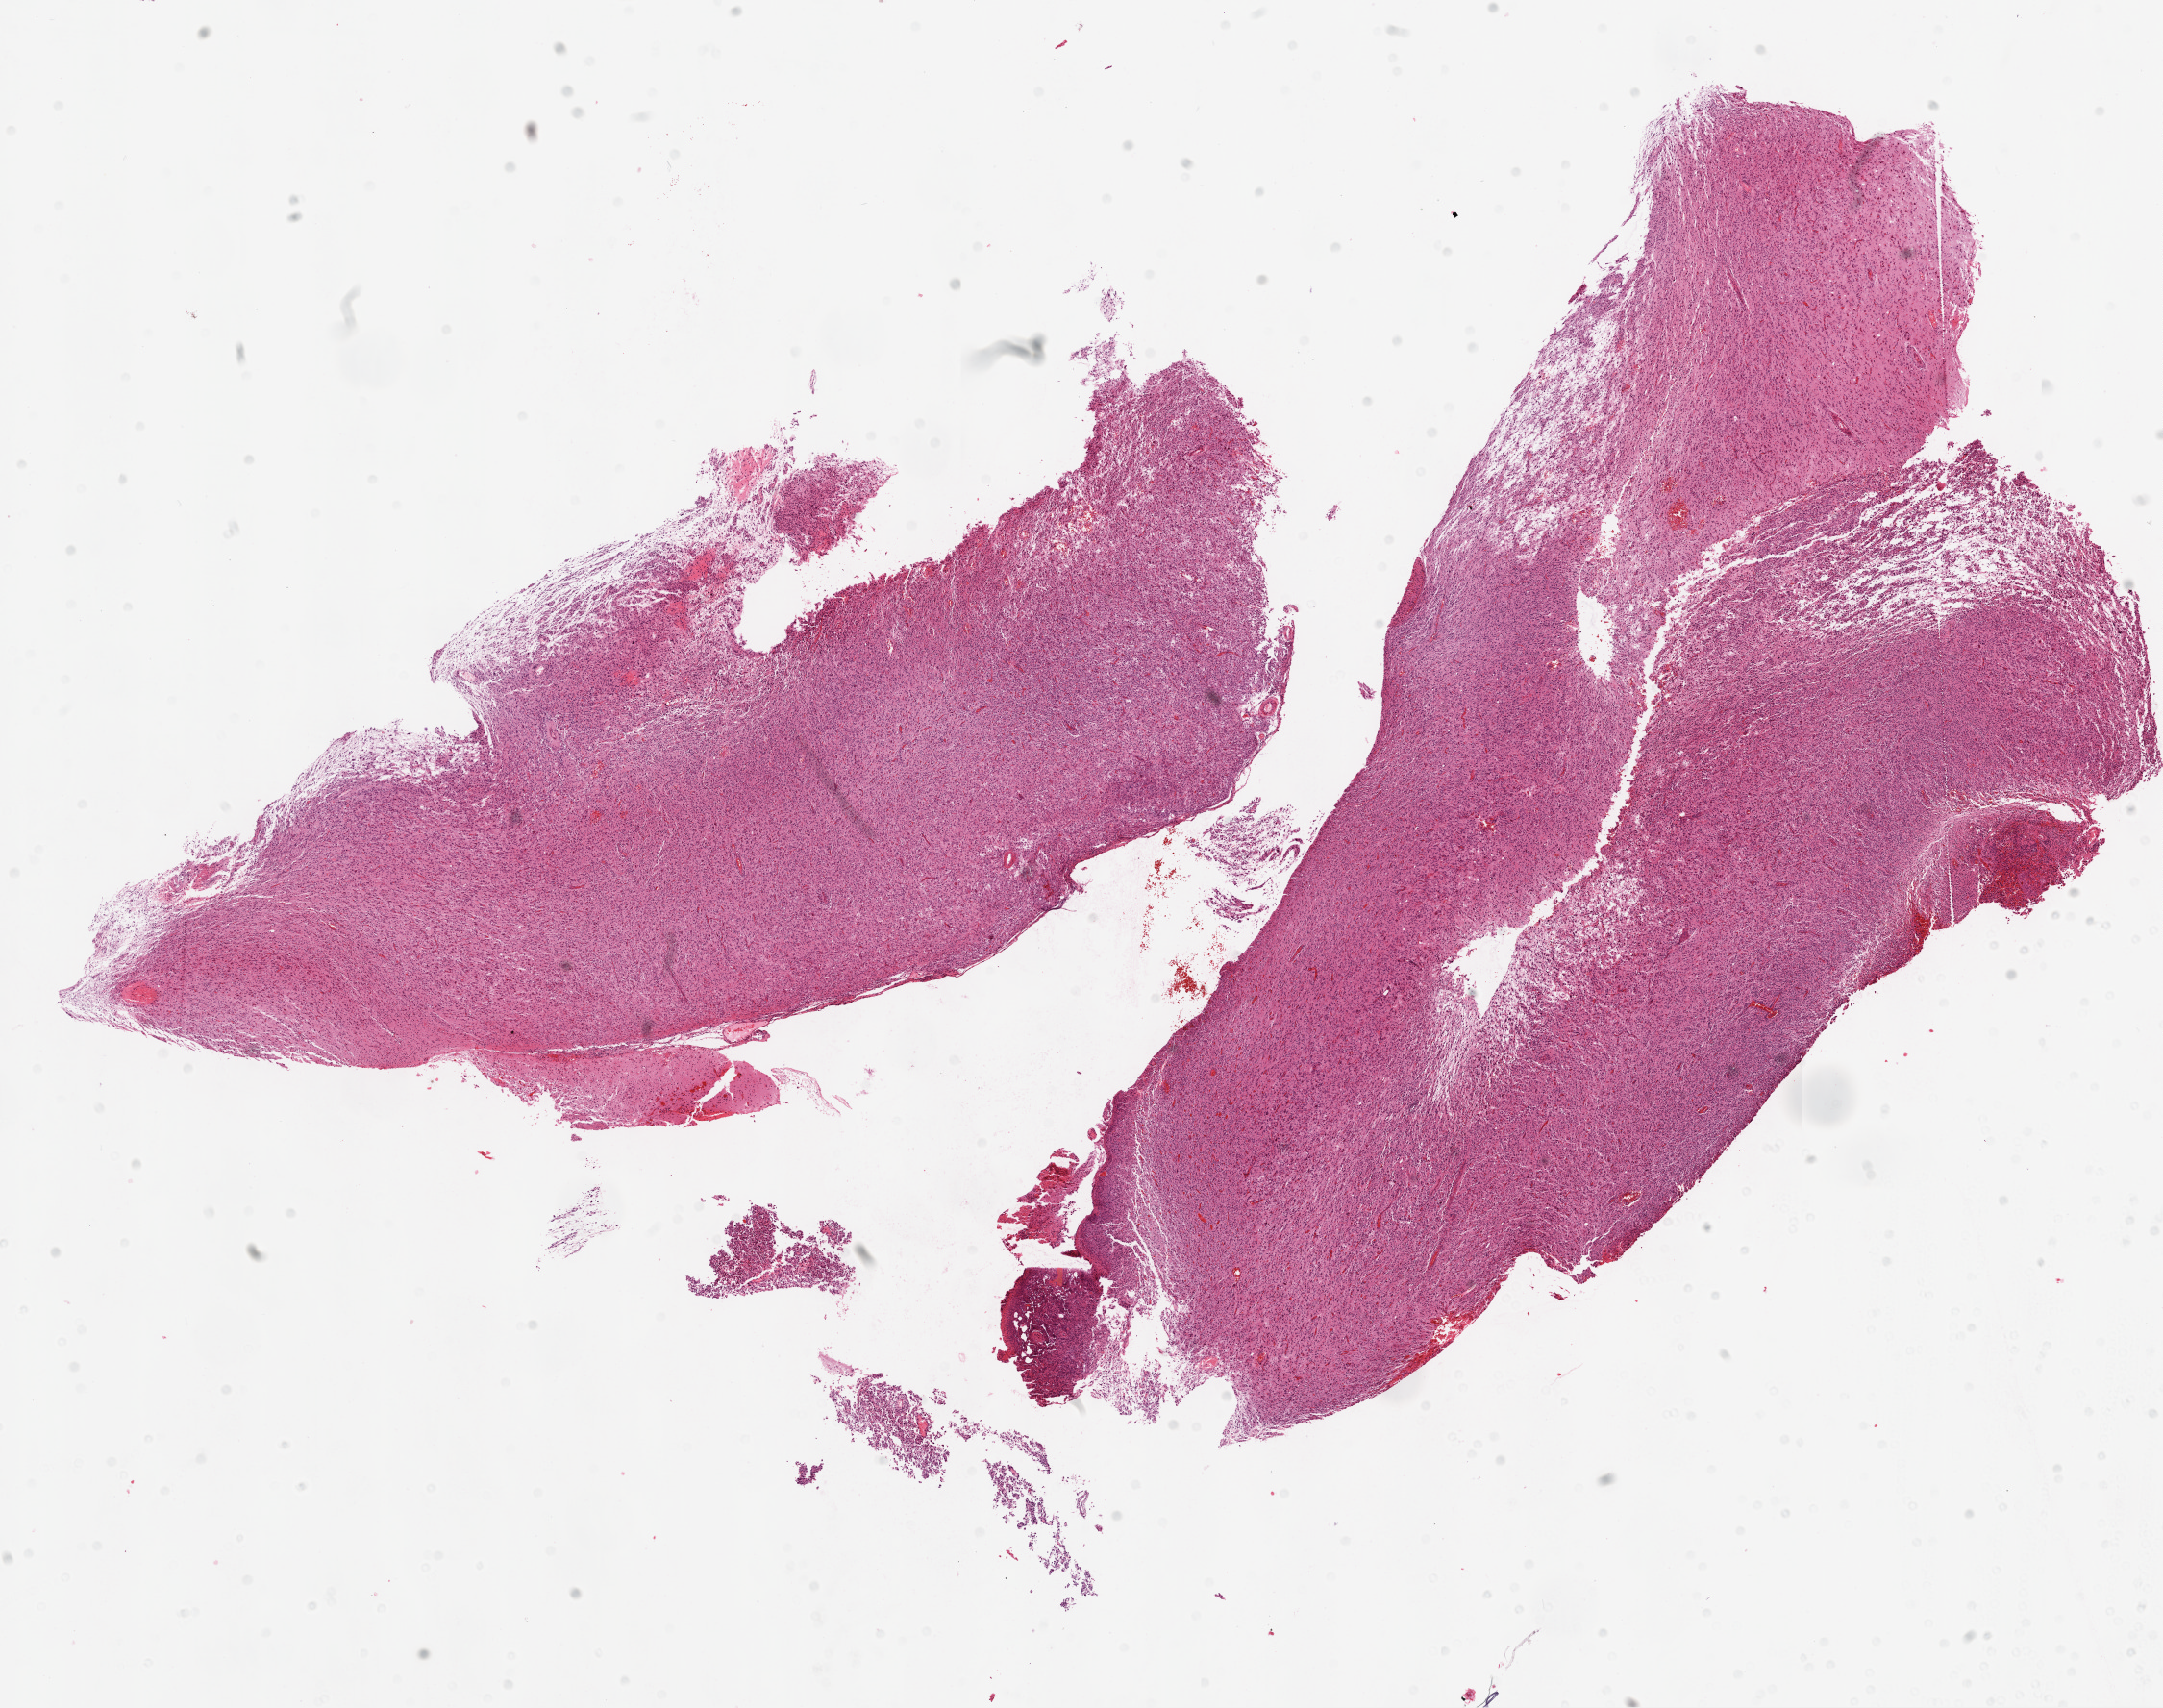
Digitized H&E-stained tissue section (whole slide), low-resolution overview of the scanned area, about 18.1 x 14.3 mm (acquisition: 20x scan), formalin-fixed paraffin-embedded (FFPE) diagnostic section, sample: primary tumour, brain. Male patient; age at initial diagnosis 17 years.
- pathologic diagnosis: Glioblastoma